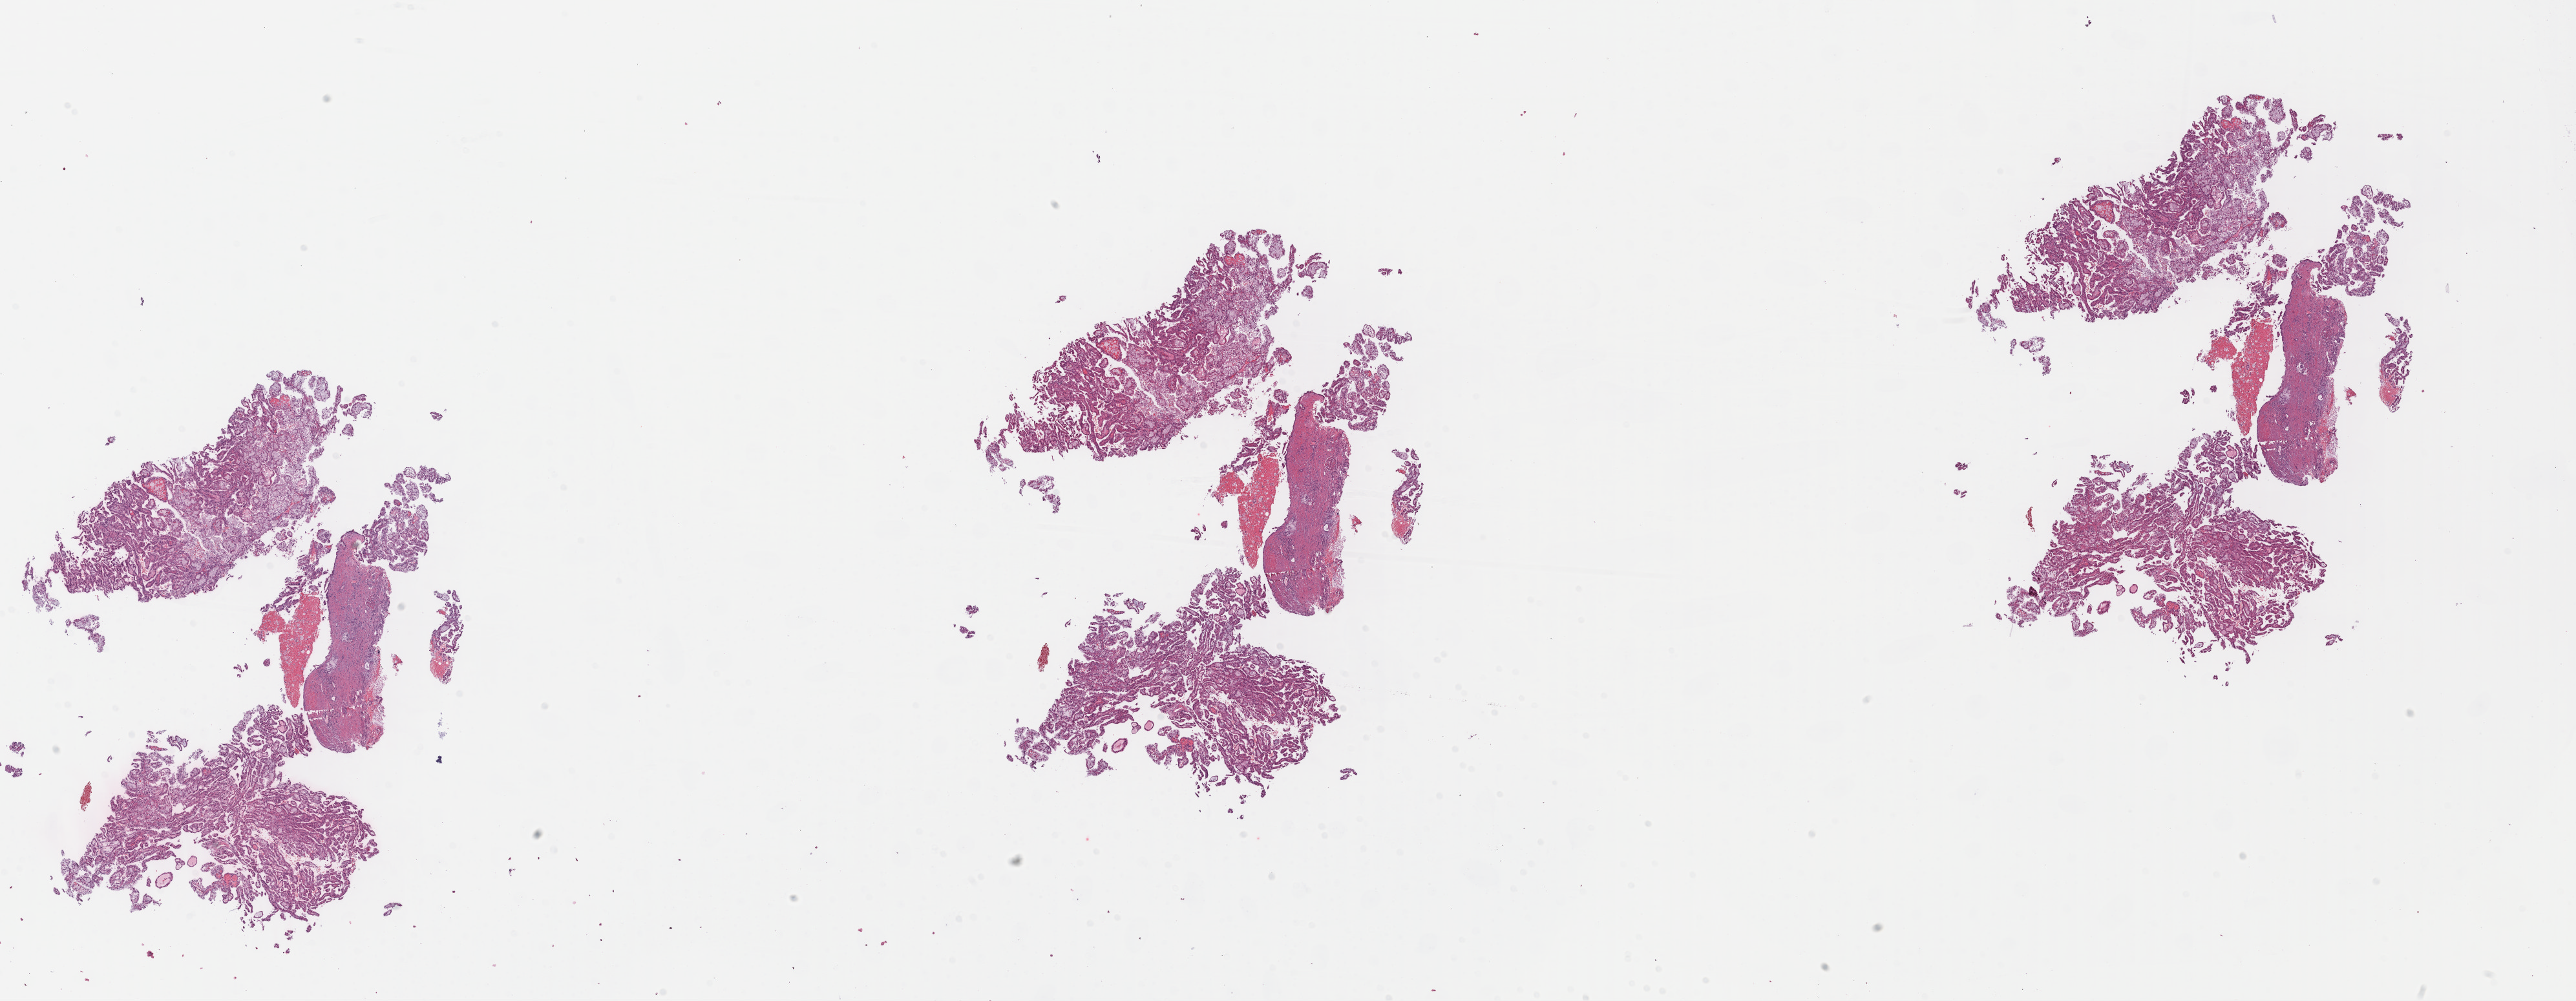
H&E-stained whole-slide image, whole scanned area (about 31.3 x 12.2 mm) shown as a low-resolution overview. Formalin-fixed paraffin-embedded (FFPE) diagnostic section. Primary tumour sample from the kidney. Male, age 43 years at initial diagnosis.
AJCC pathologic stage: I. Histologic diagnosis: Papillary adenocarcinoma, NOS.